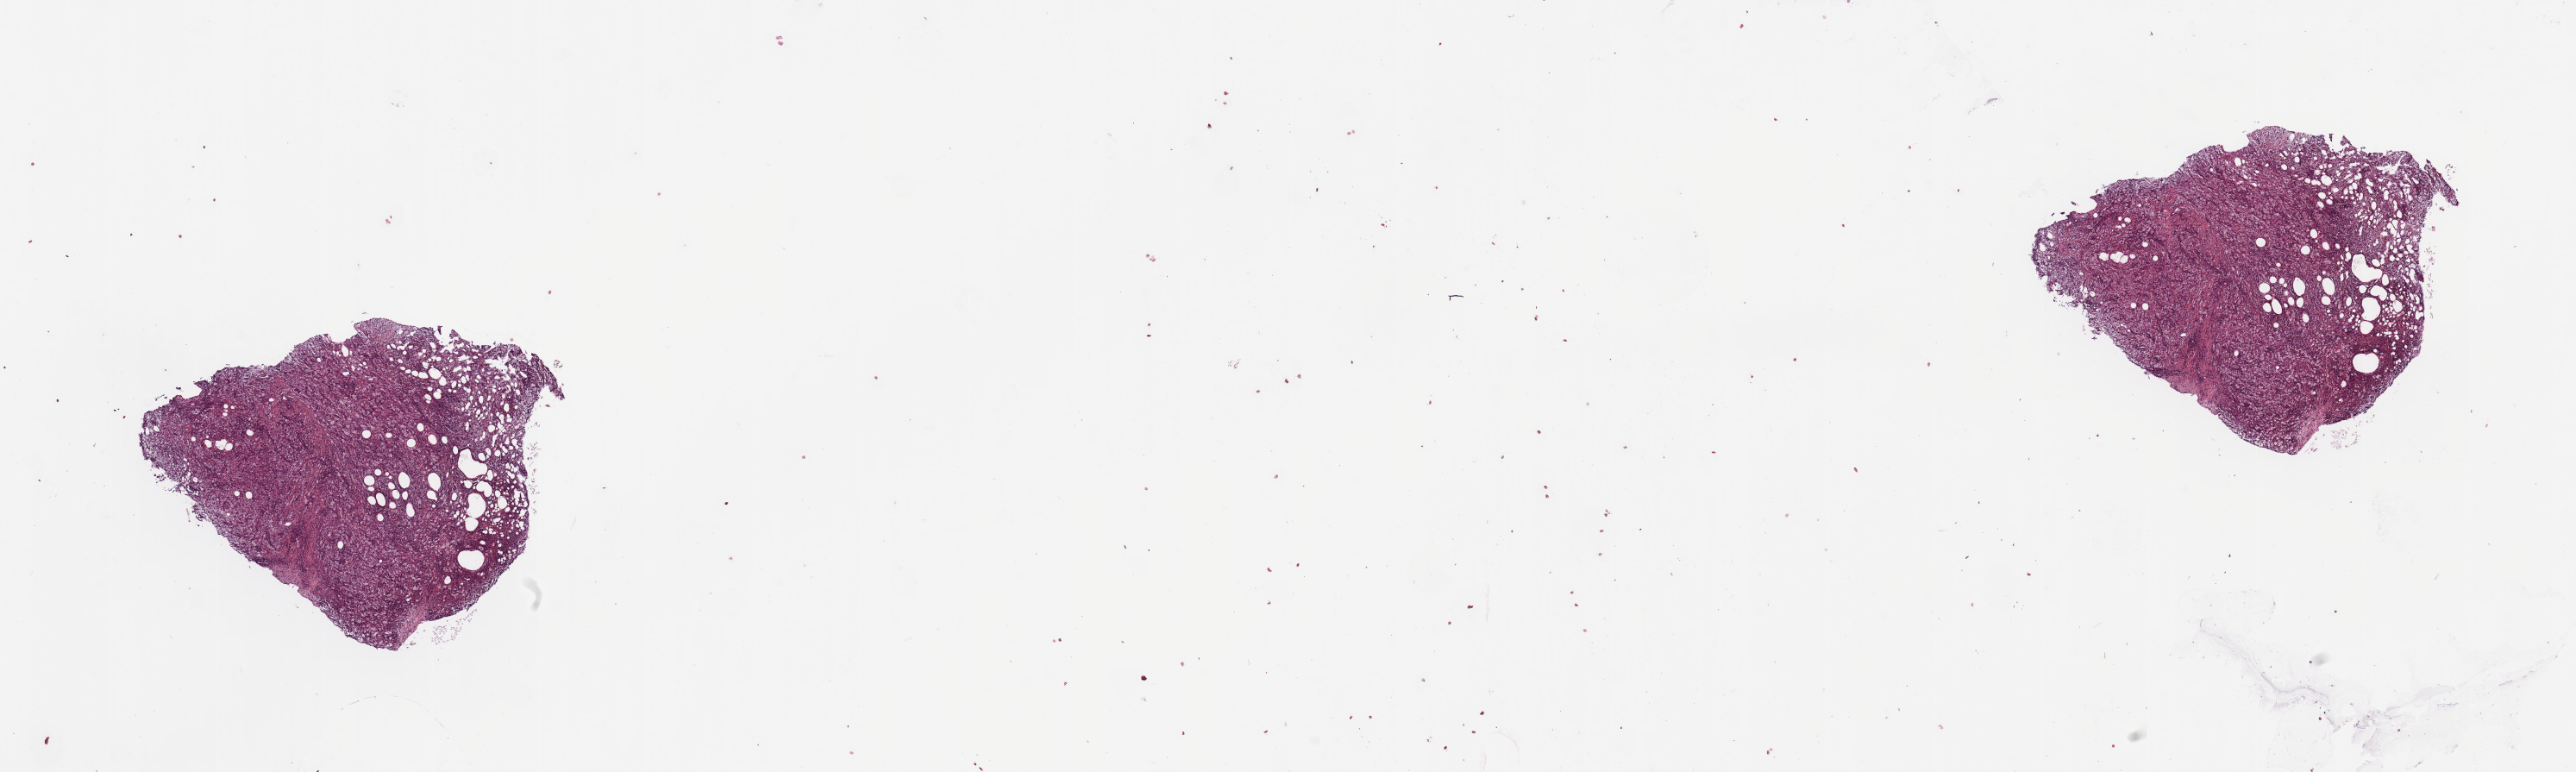
Whole-slide histology image, H&E-stained, whole scanned area (about 23.6 x 7.1 mm, slide scanned at 20x) shown as a low-resolution overview, tumour tissue sample, sampled site: kidney. Patient: male, age 69 years. Histologic grade: G2 (moderately differentiated). Composition of this section per pathologist review: tumour nuclei 90%, necrosis 0%.
* AJCC pathologic stage: II
* histologic diagnosis: Renal cell carcinoma, NOS
* primary tumour site (as recorded): middle